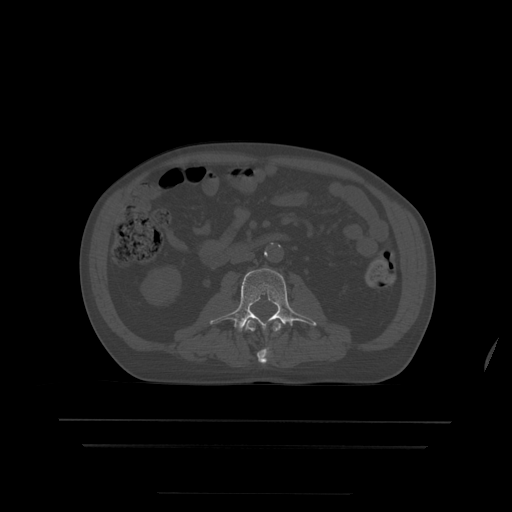
CT including the spine, one axial slice. Position 124 of 522 along the scan axis. Bone window (W 1800 / L 400 HU). 1.25 mm slice thickness. 512 × 512 image matrix, field of view 436 × 436 mm. Patient age 68 years. From the clinical record (not read from this slice): primary cancer: urothelial.
Structures marked on this image (semi-automatic segmentation, software-assisted and operator-edited):
- L2 vertebra: bounding box (x1, y1, x2, y2) in pixels: (242, 320, 282, 364)
- L3 vertebra: (210, 269, 317, 332)